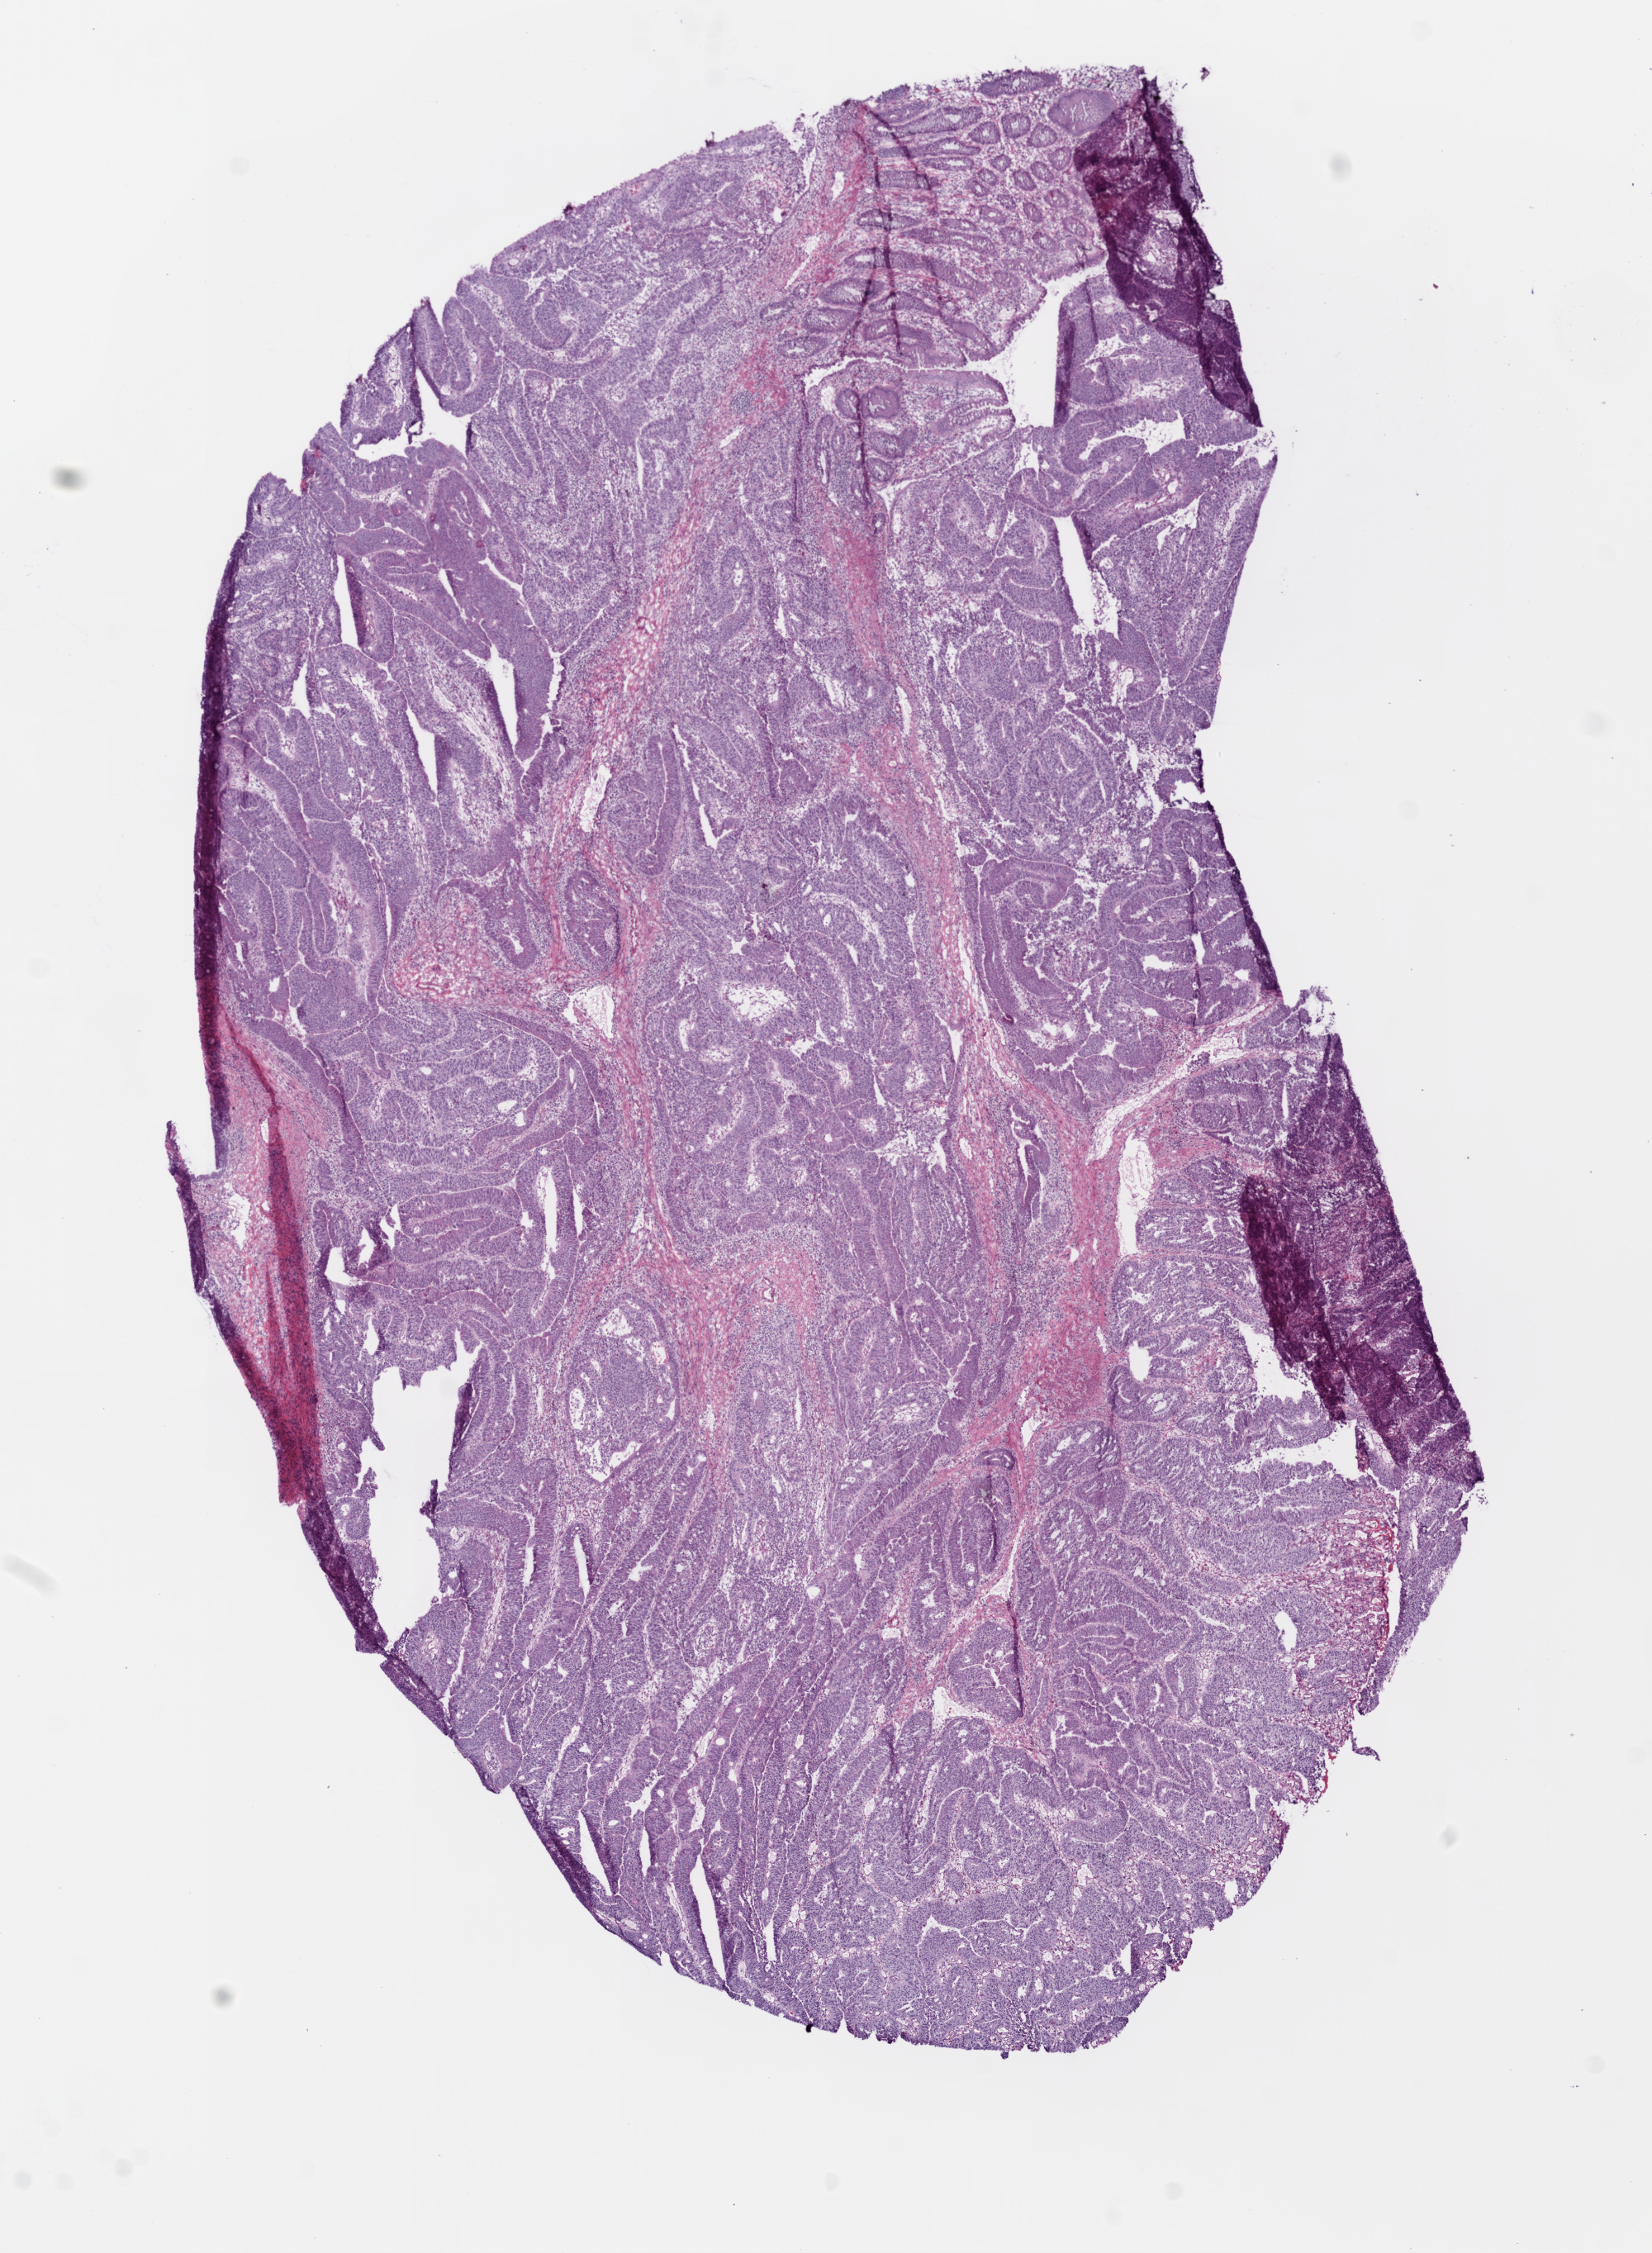
Digitized H&E-stained tissue section (whole slide), shown as a low-resolution overview of the whole scanned area (about 8.0 x 10.9 mm, from a 20x scan); frozen section from the bottom of the tissue portion; primary tumour sample from the rectum. Male, age 69 years at initial diagnosis. Composition of this section per pathologist review: tumour cells 75%, tumour nuclei 75%, normal cells 20%, stromal cells 5%, necrosis 0%. Inflammatory infiltration, as recorded: lymphocyte infiltration 50%, neutrophil infiltration 40%.
• lymph nodes positive (case pathology): 0 of 65 examined
• AJCC pathologic stage: IIA
• histologic diagnosis: Adenocarcinoma, NOS (rectosigmoid junction)